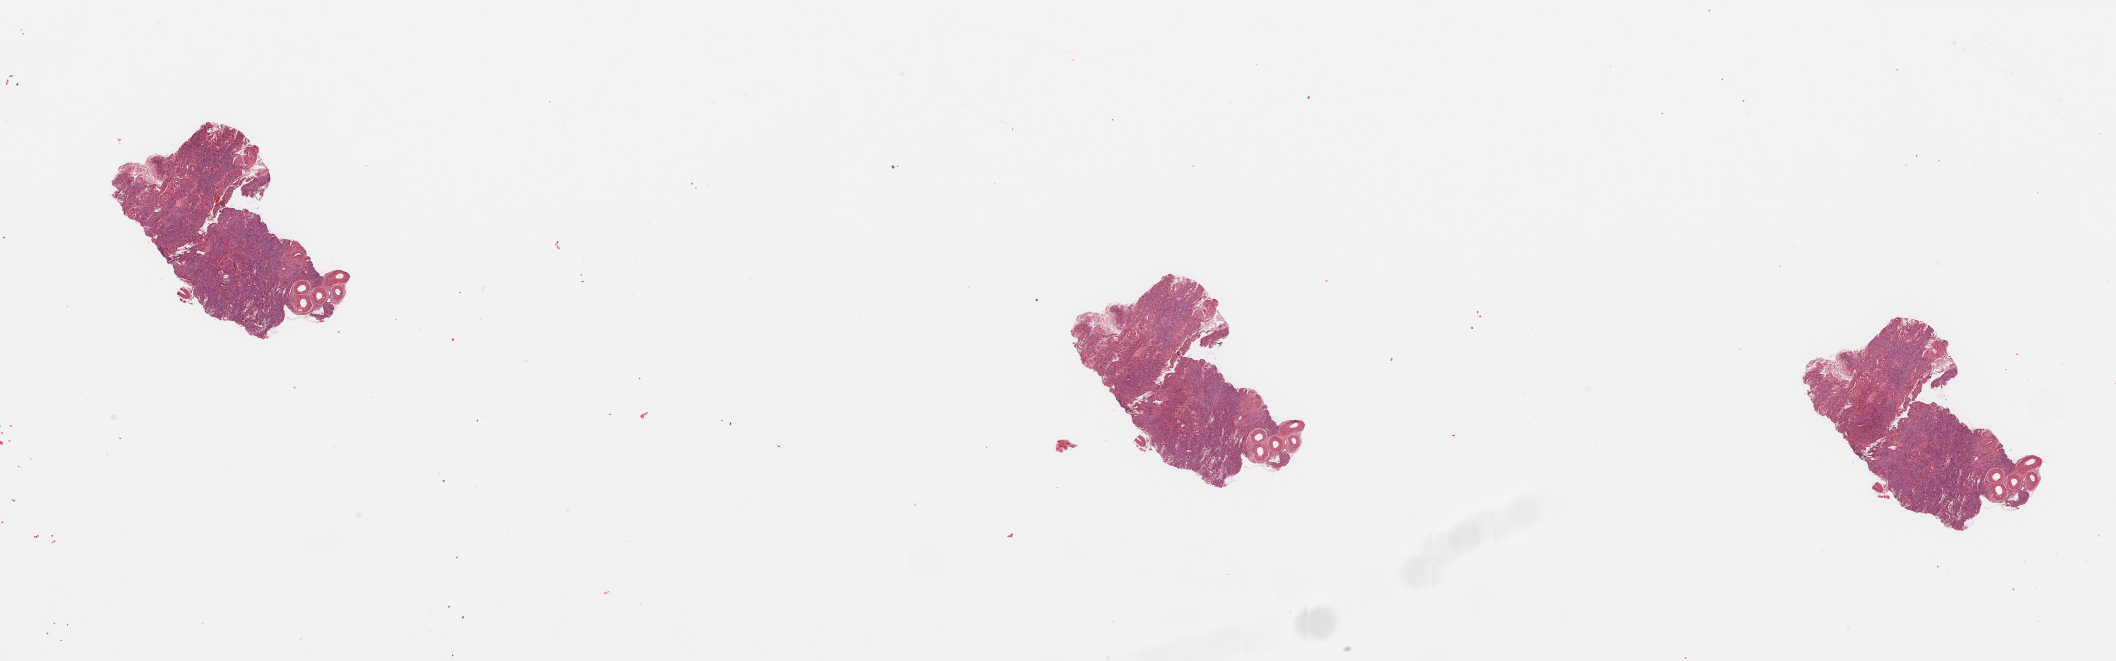
Hematoxylin and eosin (H&E) stained whole-slide image — low-resolution overview of the scanned area, about 33.5 x 10.5 mm; uterus, normal (non-tumour) tissue. Patient: female, age 77 years.
* this section: normal (non-tumour) tissue from the same patient
* patient diagnosis: Endometrioid adenocarcinoma, NOS